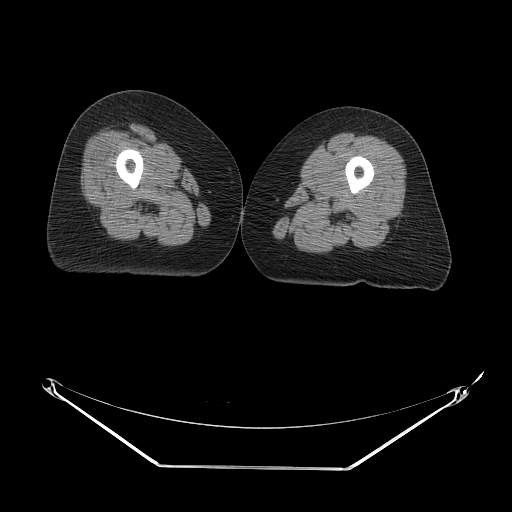
CT of an extremity soft-tissue mass (from a PET/CT study), one axial slice. 140 kVp. Soft-tissue window (W 400 / L 40 HU). 3.75 mm slice thickness. 512 × 512 image matrix, field of view 500 × 500 mm. Female patient. From the clinical record (not read from this slice): histological type: malignant solitary fibrous tumor; grade: intermediate; site of the primary tumour: right thigh.
Structures marked on this image (expert contour drawn on MRI and transferred to this co-registered scan by the dataset authors):
- gross tumour volume including surrounding oedema: bounding box [x1, y1, x2, y2] px = [139, 135, 179, 159]